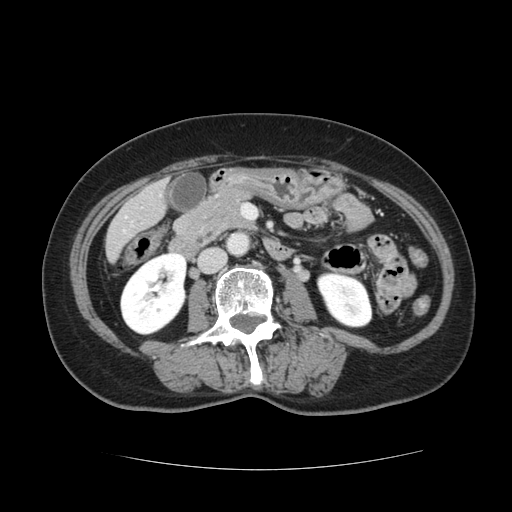
Contrast-enhanced abdominal CT, one axial slice; position 27 of 128 along the scan axis; intravenous contrast given; soft-tissue window (W 400 / L 40 HU); 2.5 mm slice thickness; 512 × 512 image matrix, field of view 366 × 366 mm. Female patient, age 67 years. Case-level facts recorded for this patient, not image findings: diagnosis: colorectal cancer liver metastases, imaged before liver resection; multiple liver metastases: yes; largest metastasis: 3 cm.
Outlined on this slice (outlined manually by an expert reader):
- liver: bounding box <107,182,166,258> (left, top, right, bottom; pixels)
- planned liver remnant (the part of the liver to remain after resection): <107,210,139,258>